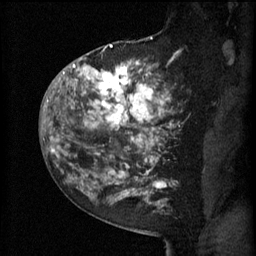
Breast MRI (dynamic contrast-enhanced), one sagittal slice; slice 38 of 60 in the series (ordered by position); 3 images stored at this slice position (order not interpretable as contrast timing); 1.5 T; TE 4.2 ms, TR 11 ms; 256 × 256 image matrix, field of view 180 × 180 mm. Female patient, age 52 years.
Structures marked on this image (semi-automatic segmentation, software-assisted and operator-edited):
- analysis volume of interest (the breast-tissue region the enhancement analysis was run in; not a lesion): bounding box <81,52,174,157> (left, top, right, bottom; pixels)
- tumour enhancement mask (voxels above the 70 % enhancement threshold inside the analysis volume of interest): <83,54,173,155>